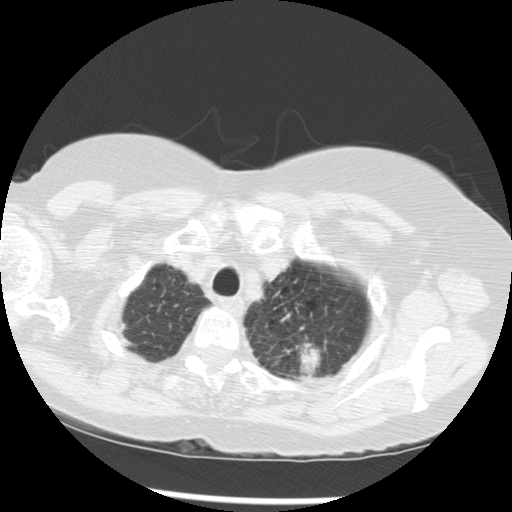
Chest CT (low-dose screening protocol), one axial image; third annual screen; lung window (W 1500 / L -600 HU); 2.5 mm slice thickness; standard (soft-tissue) reconstruction kernel (STANDARD); slice 247 of 283 in the series; 512 × 512 image matrix. Female participant, aged 70 years at enrolment.
Expert reader's lesion annotation, box from (x=244, y=295) to (x=344, y=382) px. Screening reader's record for this exam (one nodule recorded; not confirmed to be the boxed lesion): non-calcified nodule or mass ≥4 mm, left upper lobe, 32 × 26 mm, spiculated (stellate) margins, soft tissue attenuation, pre-existing on the prior screen: yes; interval growth: yes. Official screen result: positive, other. Participant outcome: lung cancer diagnosed 24 days after this screen — neoplasm, malignant, left upper lobe, stage IIIB (AJCC 6th edition), 40 mm at pathology.